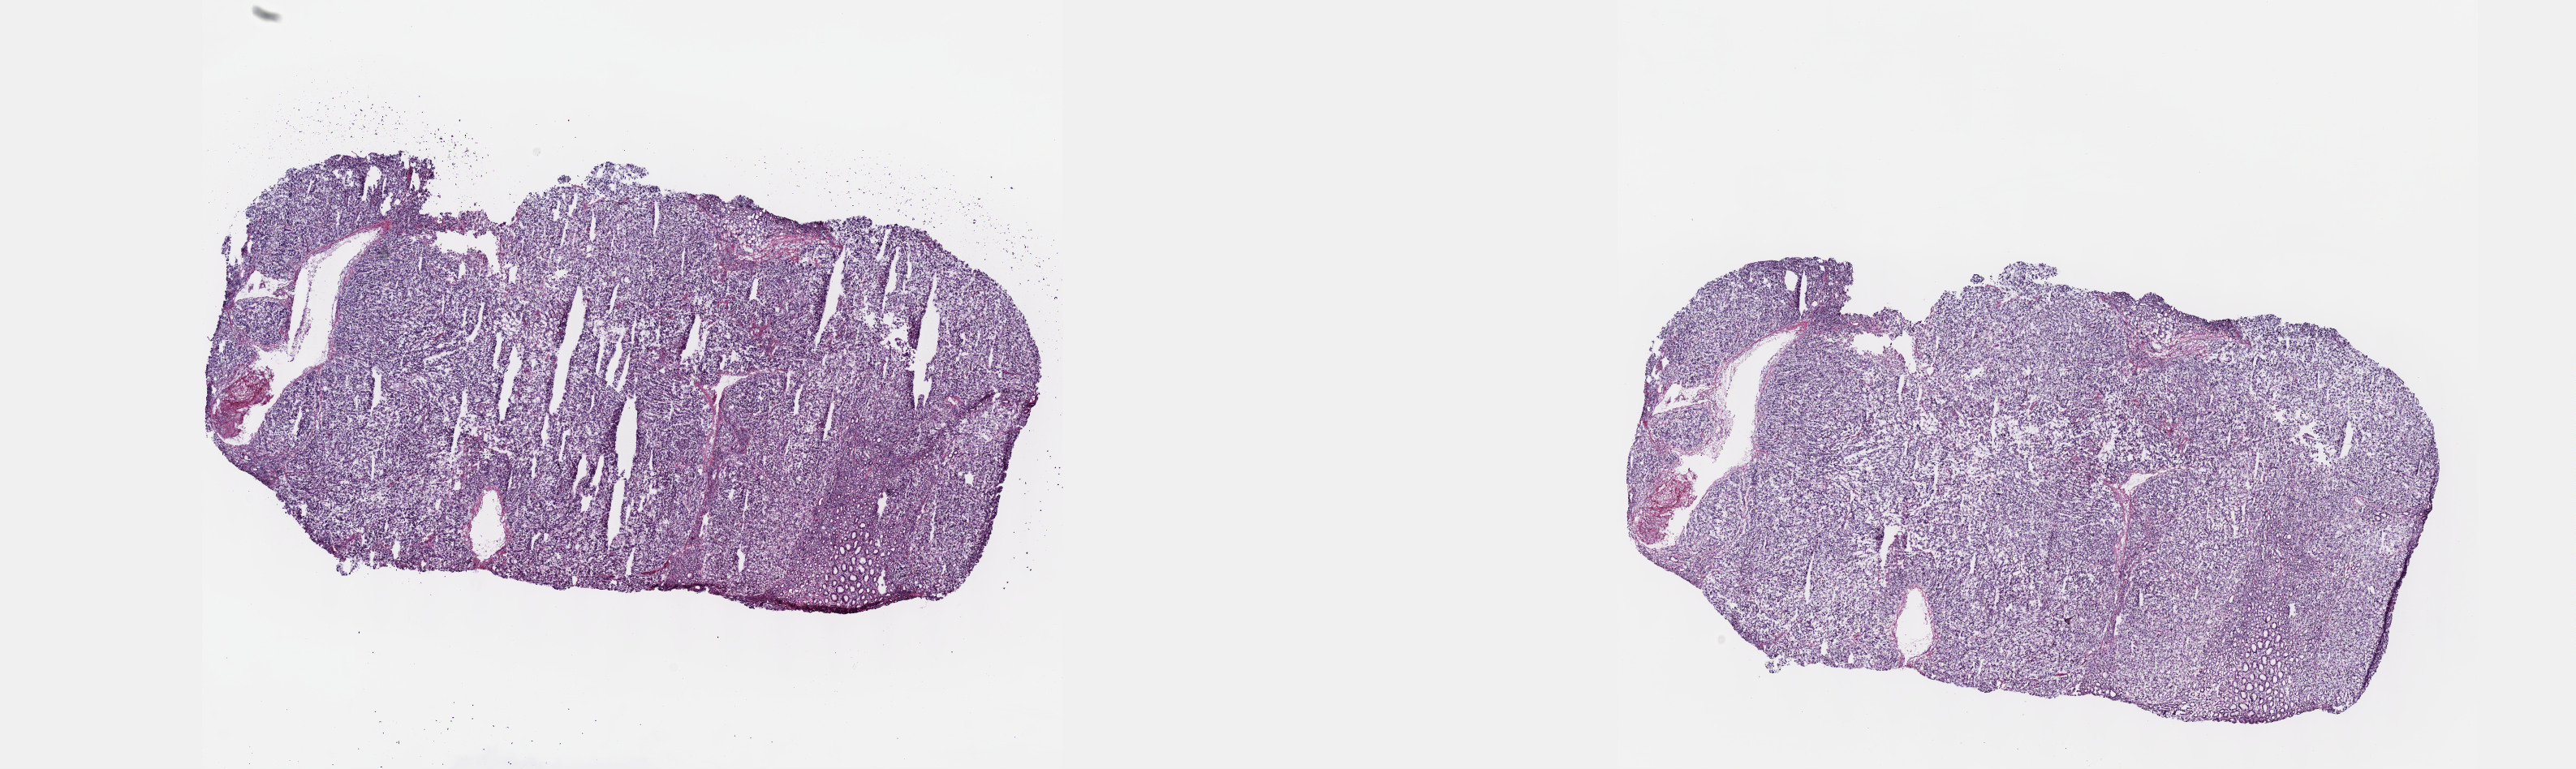
H&E whole-slide image, a low-resolution overview of the entire scanned area, about 25.7 x 7.7 mm; frozen section from the top of the tissue portion; sample: primary tumour, stomach. Male patient; age at initial diagnosis 73 years. Histologic grade: G3 (poorly differentiated). Slide review estimates, as recorded: tumour cells 75%, tumour nuclei 90%, normal cells 10%, stromal cells 10%, necrosis 5%. Infiltration values recorded for this section: lymphocyte infiltration 8%, monocyte infiltration 1%, neutrophil infiltration 1%.
AJCC pathologic stage: IIIB (6th edition). Pathologic diagnosis: Carcinoma, diffuse type (cardia, NOS).